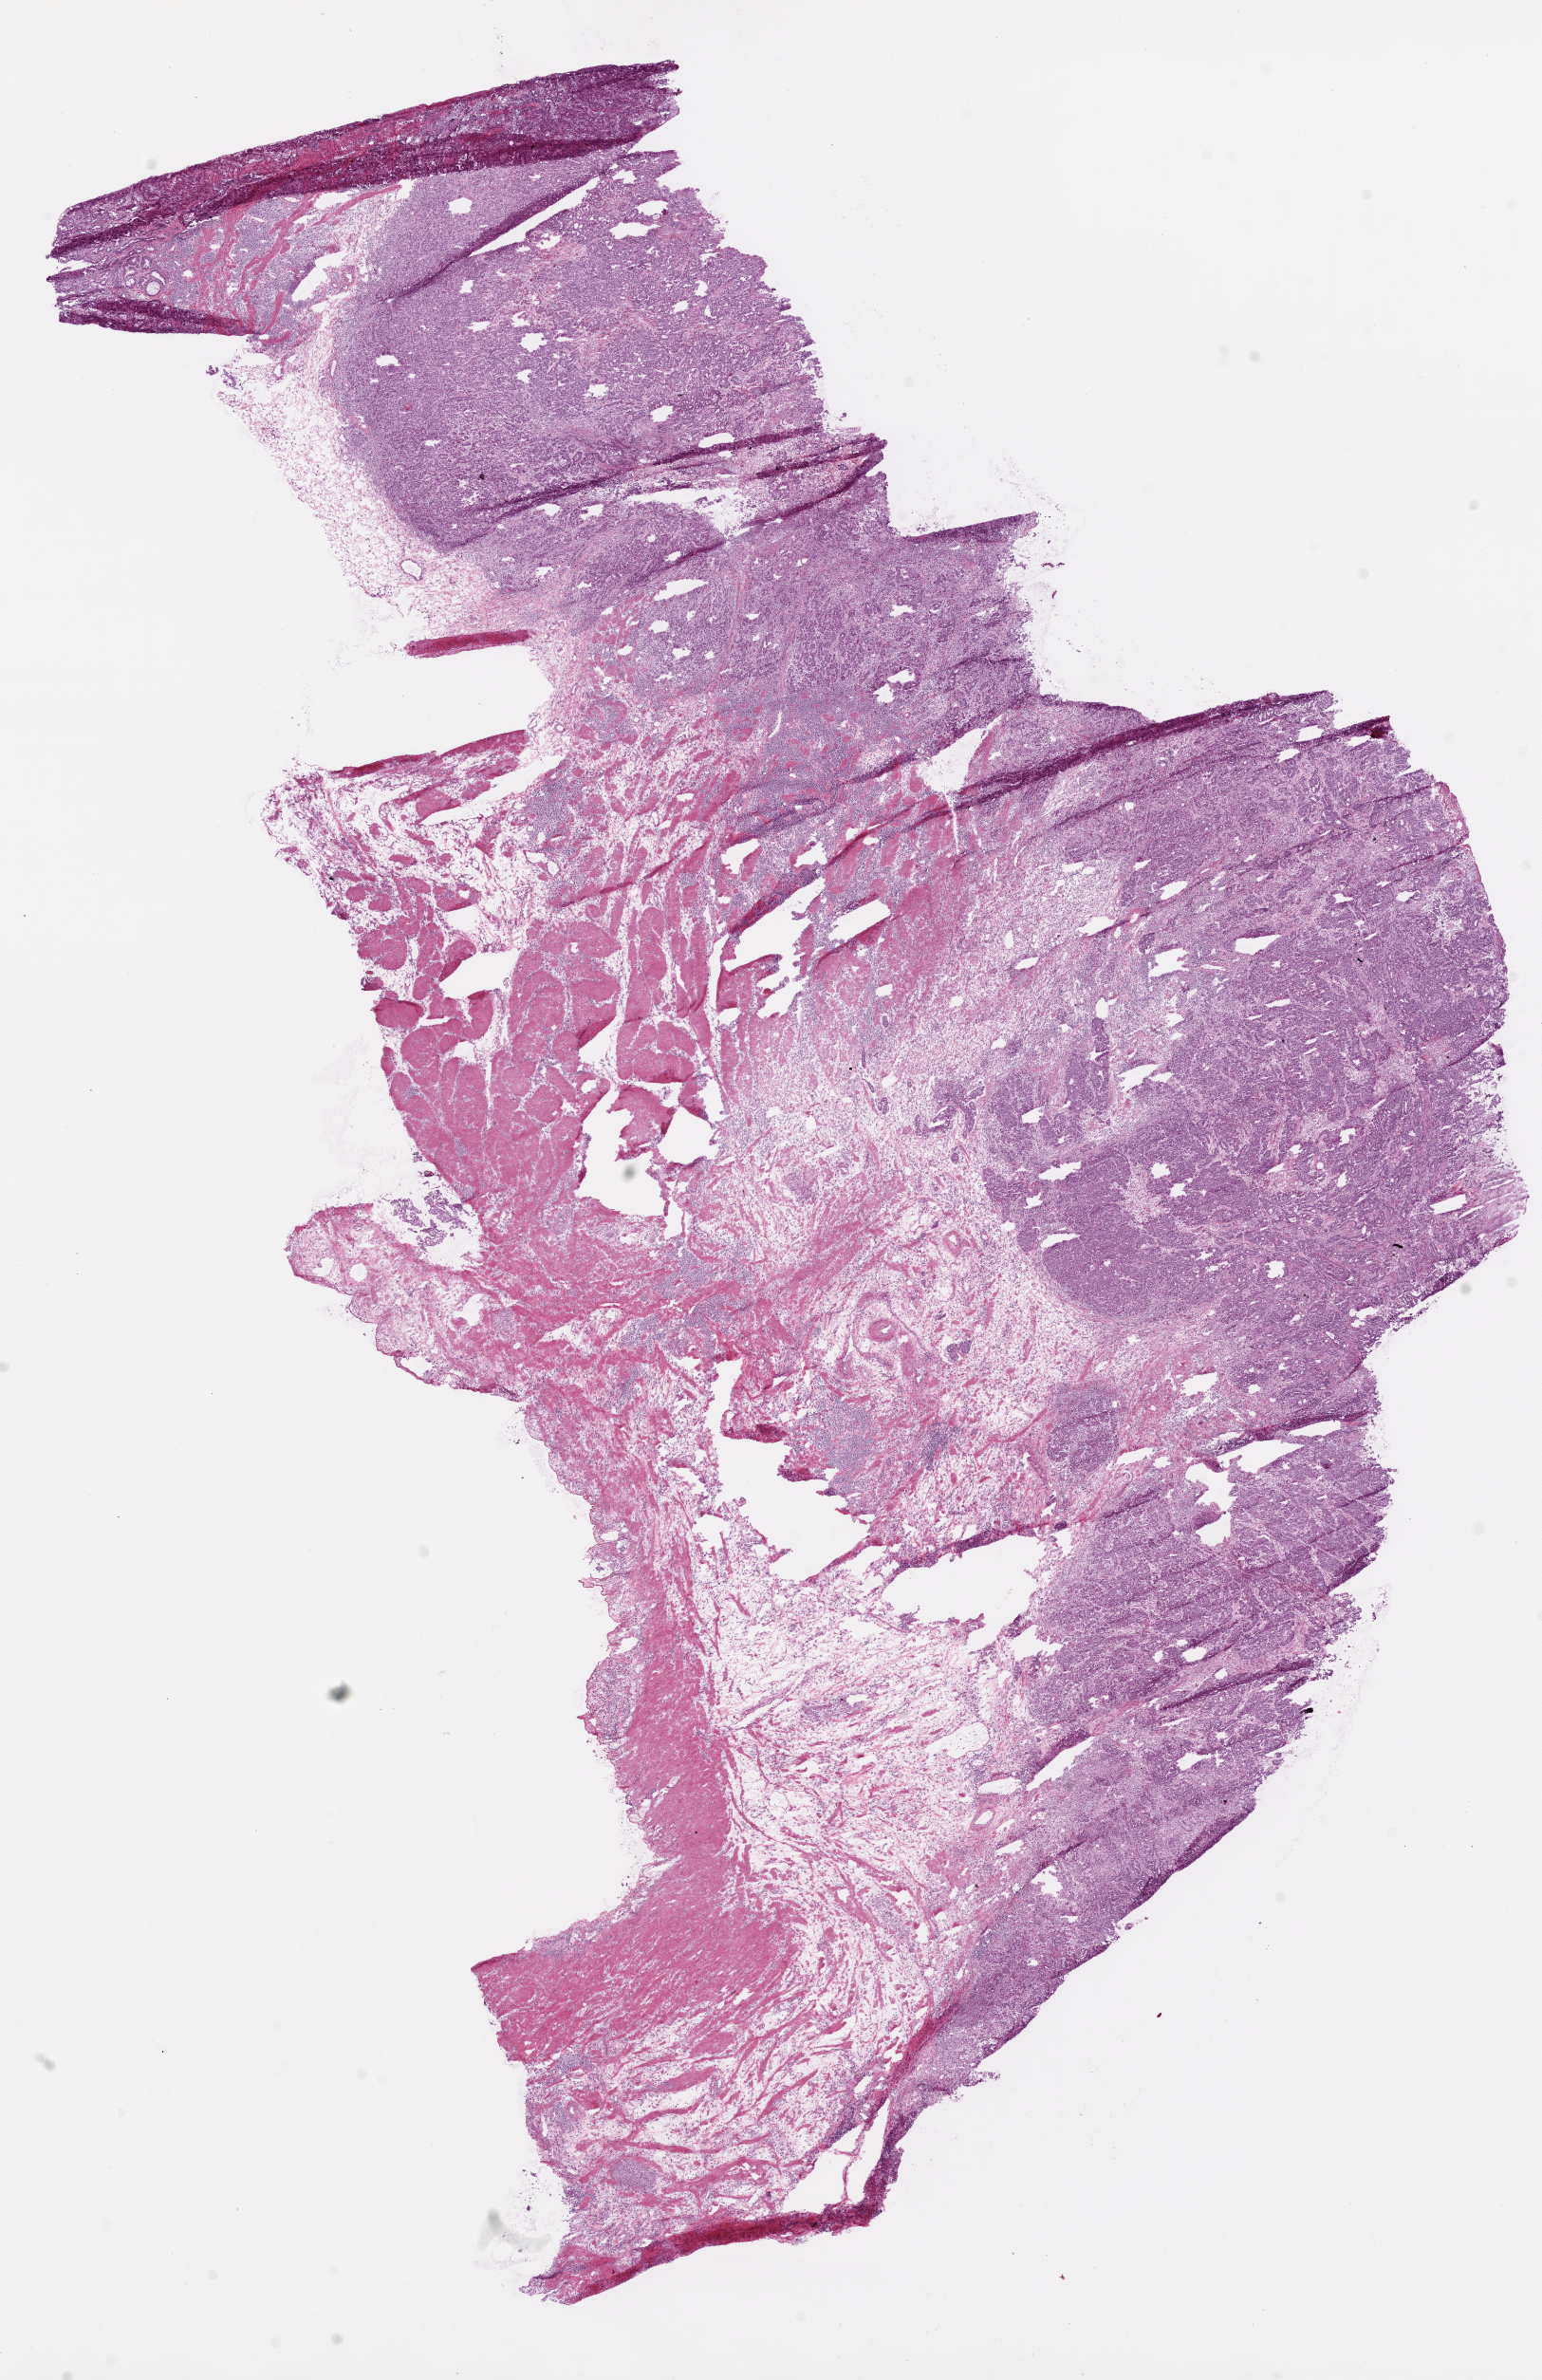
Hematoxylin and eosin (H&E) stained whole-slide image, whole scanned area (about 13.0 x 20.1 mm, from a 20x scan) shown as a low-resolution overview. Frozen section from the top of the tissue portion. Stomach, primary tumour sample. Patient: male, age at initial diagnosis 80 years. Histologic grade: G2 (moderately differentiated). Composition of this section per pathologist review: tumour cells 69%, tumour nuclei 80%, normal cells 5%, stromal cells 25%, necrosis 1%.
Pathologic diagnosis: Adenocarcinoma, NOS (gastric antrum).